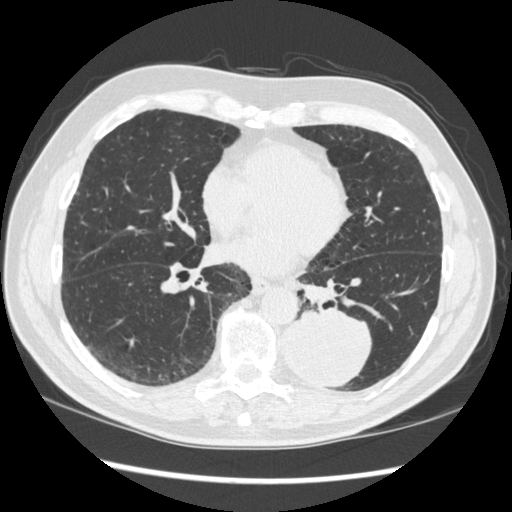
Chest CT (low-dose screening protocol), one axial image; first (baseline) screen; lung window (W 1500 / L -600 HU); 1.25 mm slice thickness; slice 139 of 348 in the series; 512 × 512 image matrix, field of view 360 × 360 mm. Male participant, aged 72 years at enrolment. Current smoker at enrolment.
Expert-annotated lung lesion, bounding box <270,300,374,390> (left, top, right, bottom; pixels). The screening reader recorded 2 non-calcified nodules or masses ≥4 mm on this exam (left lower lobe, right middle lobe); which of them this box marks is not recorded. Official screen result: positive, change unspecified: nodule(s) >= 4 mm or enlarging nodule(s), mass(es), or other non-specific abnormalities suspicious for lung cancer. Lung cancer was diagnosed 37 days after this screen: squamous cell carcinoma, NOS, left lower lobe, stage IIIA (AJCC 6th edition), 60 mm at pathology.